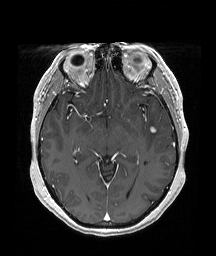
Brain MRI from a brain-tumour surgery series, one axial slice; slice 111 of 192 in the series (ordered by position); T1-weighted post-contrast; 1 mm slice thickness; 216 × 256 image matrix, field of view 211 × 250 mm. Case-level facts recorded for this patient, not image findings: histopathology: Papillary glioneuronal tumor; WHO grade: 1; tumour location: Left Temporal.
Structures marked on this image (outlined manually by an expert reader):
- tumour: bounding box <150,127,156,132> (left, top, right, bottom; pixels)